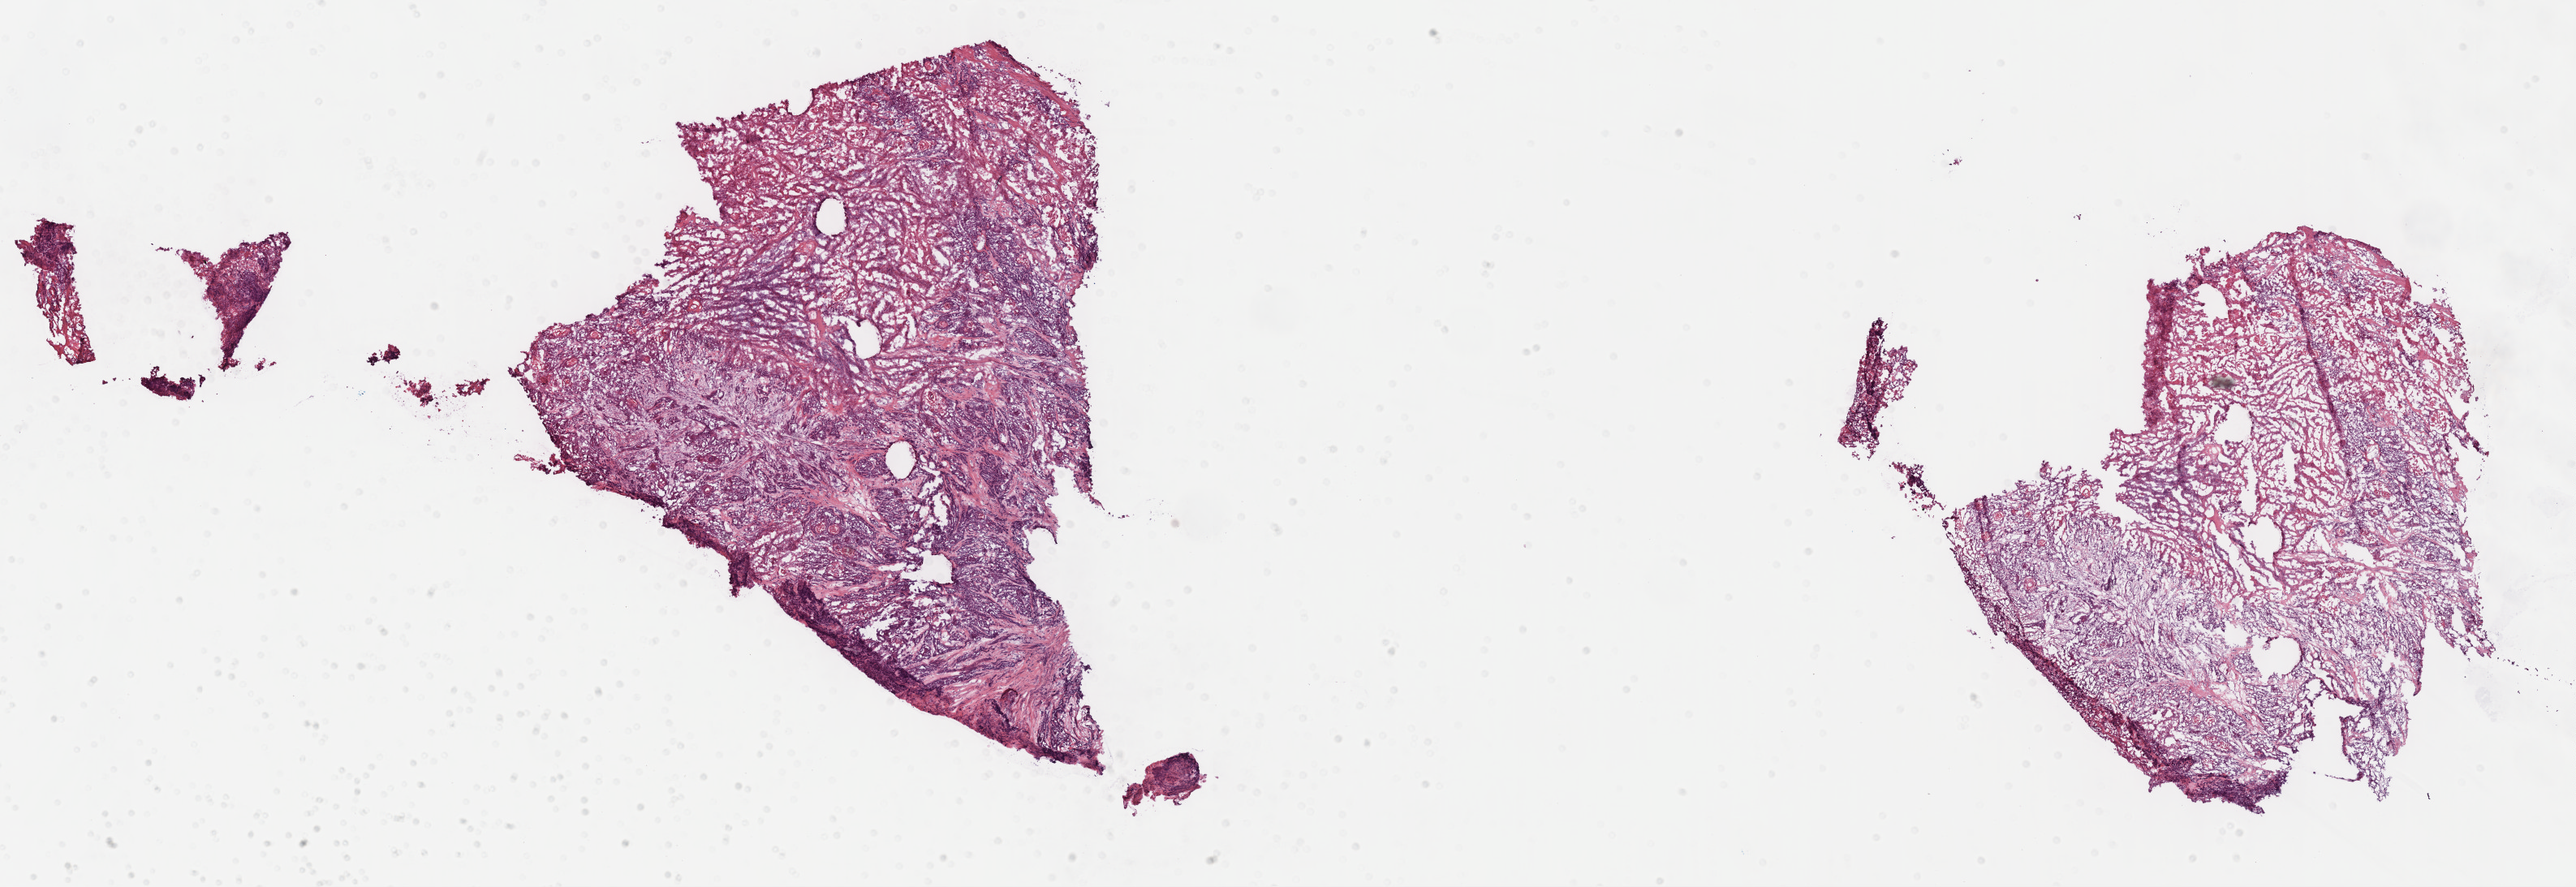
Whole-slide histology image, H&E-stained — a low-resolution overview of the entire scanned area, about 25.7 x 8.8 mm (slide scanned at 40x); frozen section; head and neck, primary tumour sample. Patient: male, age at initial diagnosis 49 years. Histologic grade: G3 (poorly differentiated). Slide review estimates, as recorded: tumour cells 85%, tumour nuclei 70%, normal cells 0%, stromal cells 10%, necrosis 5%.
• AJCC pathologic stage: III (7th edition)
• pathologic diagnosis: Squamous cell carcinoma, NOS (overlapping lesion of lip, oral cavity and pharynx)